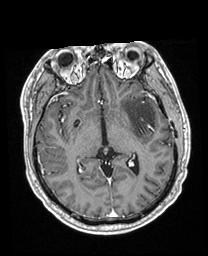
Brain MRI from a brain-tumour surgery series, one axial slice. Position 113 of 208 along the scan axis. T1-weighted post-contrast. 1 mm slice thickness. 208 × 256 image matrix. Case-level facts recorded for this patient, not image findings: histopathology: Astrocytoma; WHO grade: 3; IDH mutation: yes; tumour location: Left Insular.
Annotated regions visible in this slice (outlined manually by an expert reader):
- previous resection cavity: bounding box <149,125,156,132> (left, top, right, bottom; pixels)